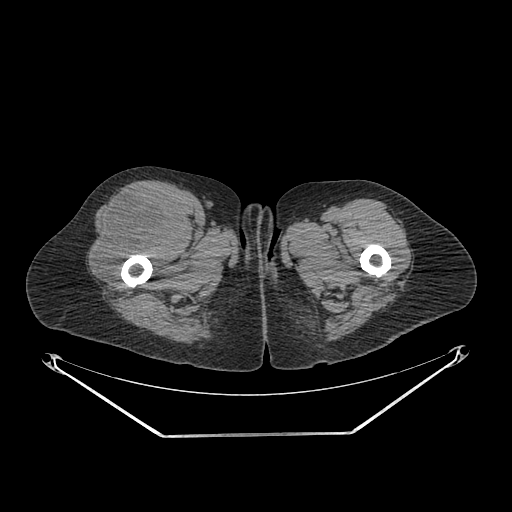
CT of an extremity soft-tissue mass (from a PET/CT study), one axial slice. Slice 269 of 311 in the series (ordered by position). Soft-tissue window (W 400 / L 40 HU). 512 × 512 image matrix, field of view 500 × 500 mm. Female patient. Case-level facts recorded for this patient, not image findings: histological type: pleiomorphic undifferentiated sarcoma; grade: high; site of the primary tumour: right quadricep.
Outlined on this slice (expert contour drawn on MRI and transferred to this co-registered scan by the dataset authors):
- tumour plus oedema (research contour): box from (x=94, y=190) to (x=184, y=275) px
- tumour (research contour): (x=94, y=190)–(x=184, y=275)